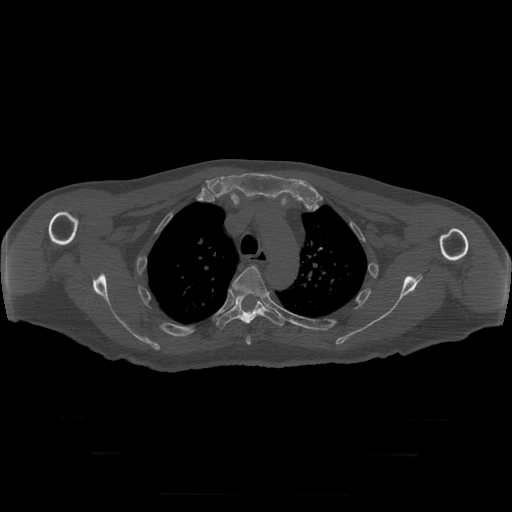
CT including the spine, one axial slice; position 233 of 397 along the scan axis; reconstruction kernel STANDARD; 120 kVp; bone window (W 1800 / L 400 HU); 1.25 mm slice thickness; 512 × 512 image matrix, field of view 510 × 510 mm. Patient age 73 years. Case-level facts recorded for this patient, not image findings: primary cancer: prostate.
Annotated regions visible in this slice (semi-automatically segmented with operator editing):
- T4 vertebra: box from (x=232, y=266) to (x=267, y=345) px
- T5 vertebra: (x=217, y=294)–(x=285, y=329)